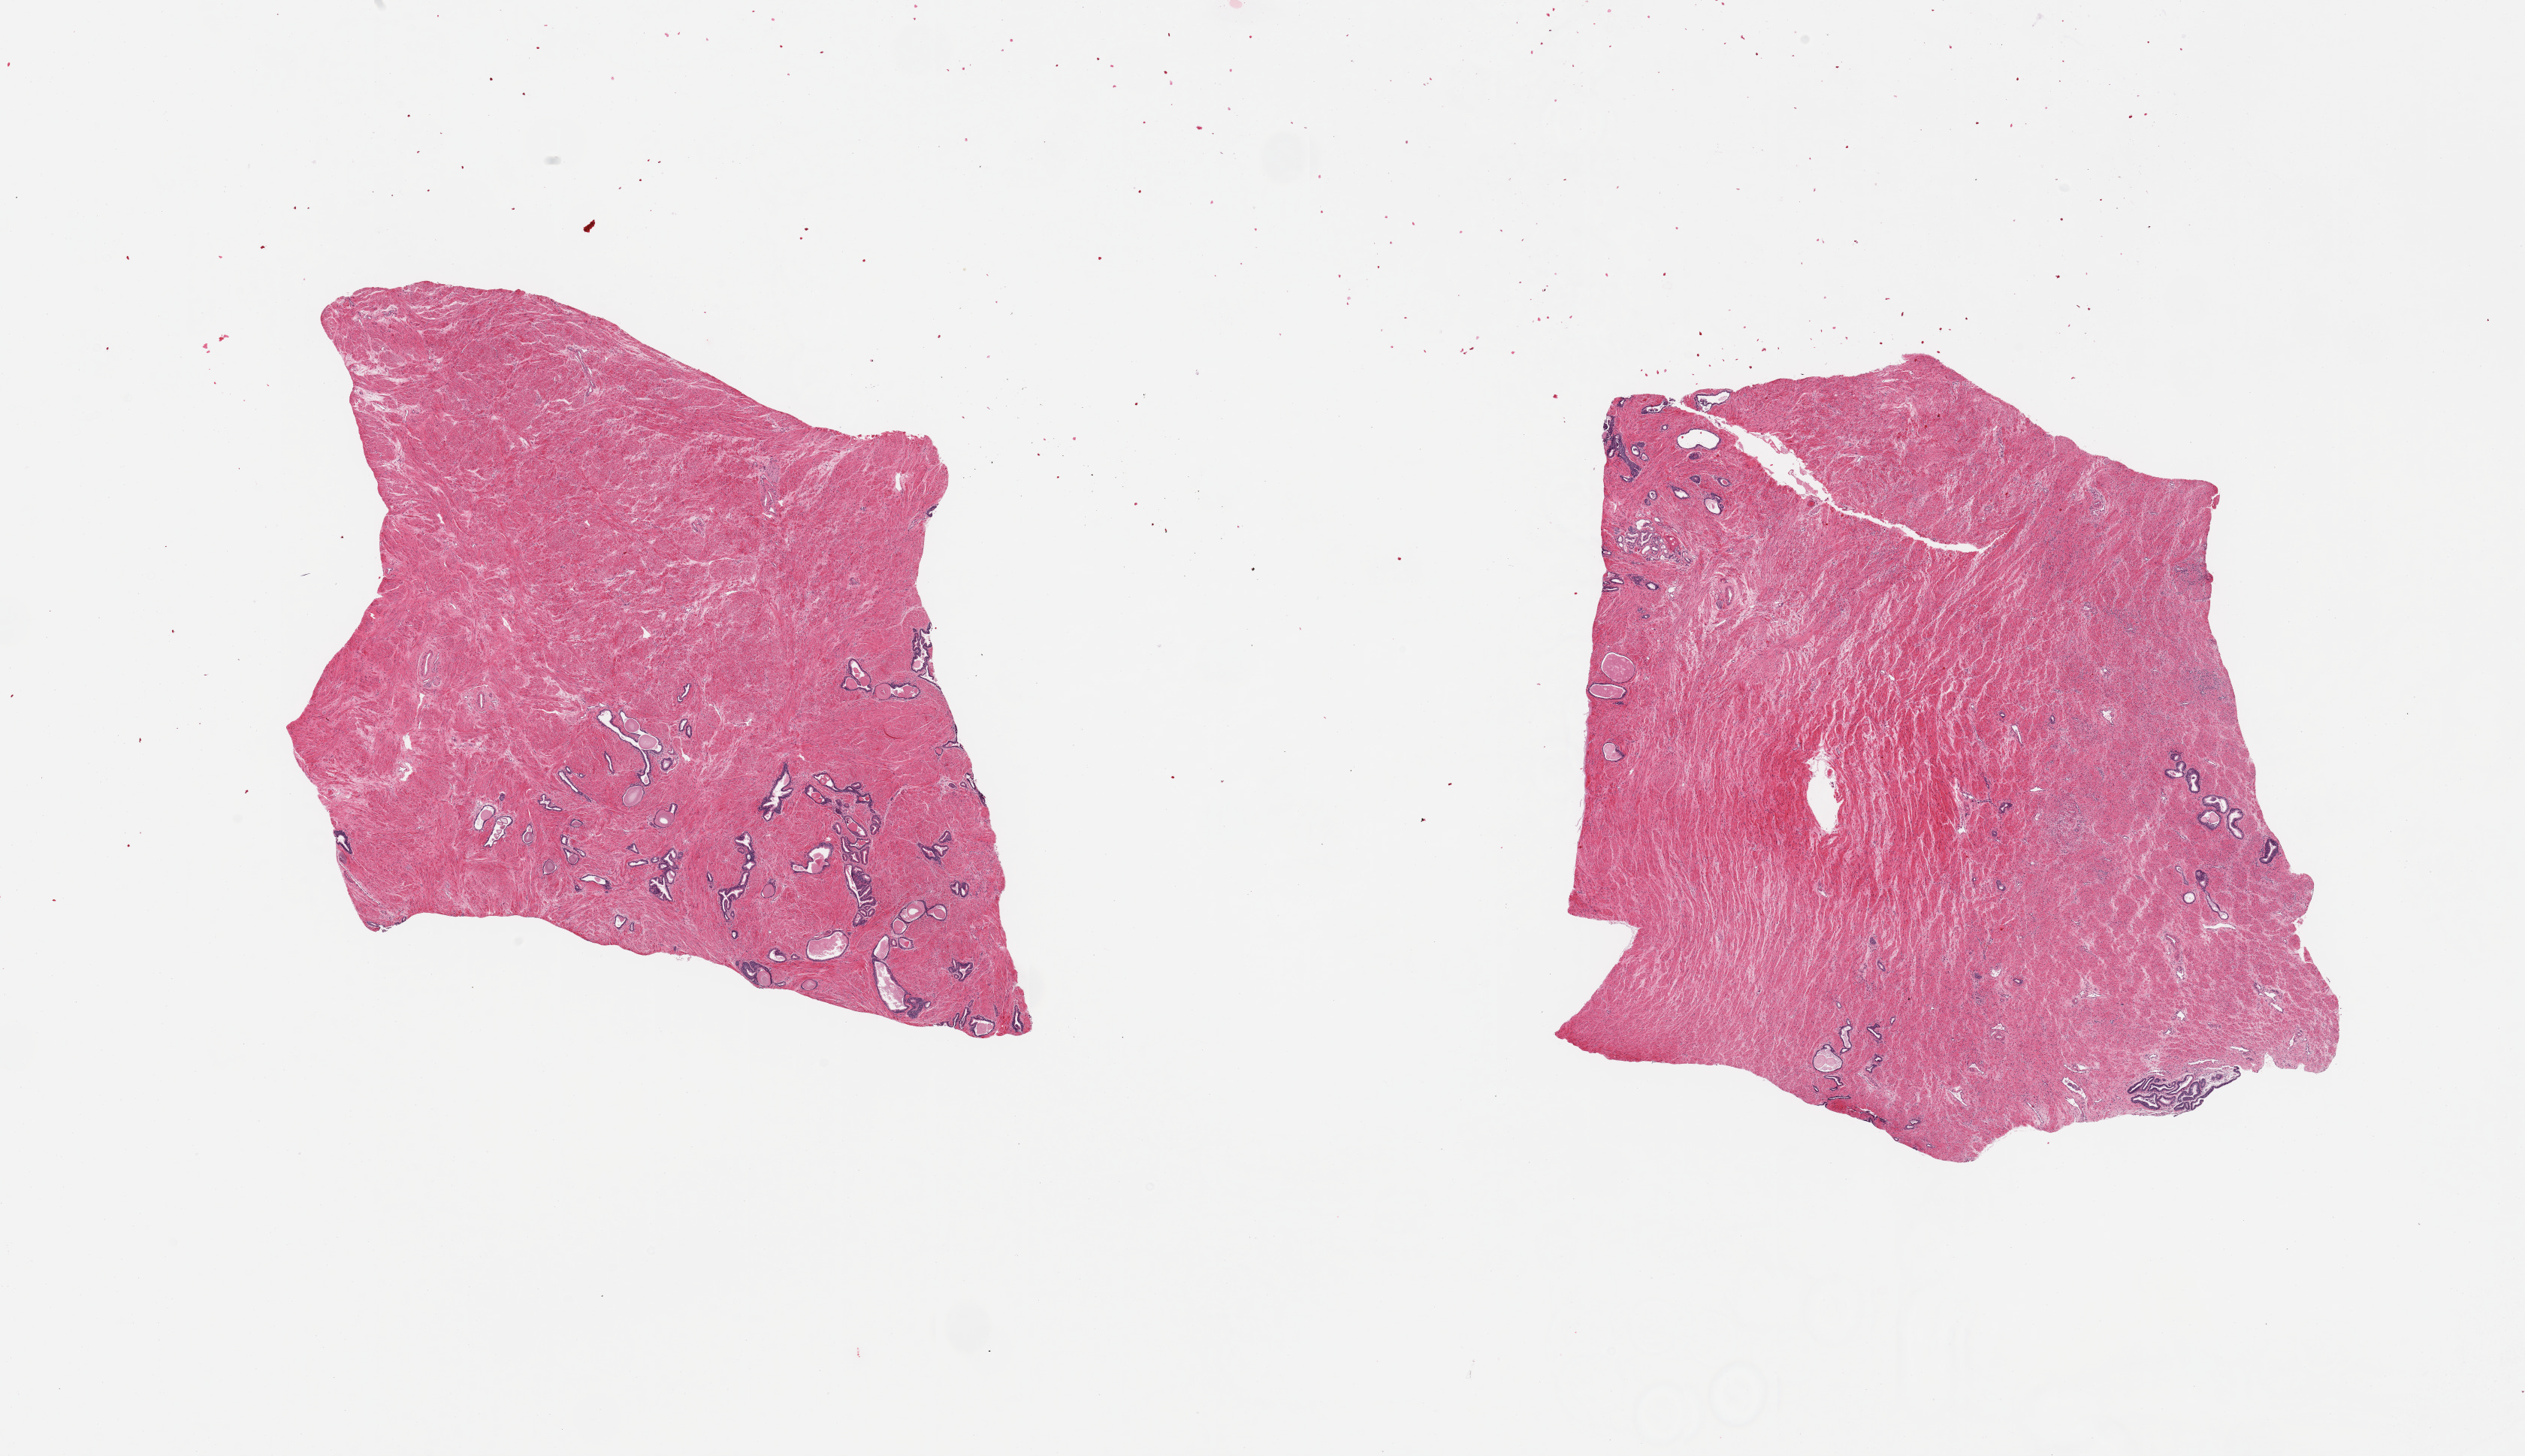
H&E whole-slide image, whole scanned area (about 26.6 x 15.3 mm, slide scanned at 20x) shown as a low-resolution overview; PAXgene-fixed, paraffin-embedded tissue; target tissue: prostate; donor tissue sample.
* review note (as recorded): 2 pieces; largely stromal; well preserved glands